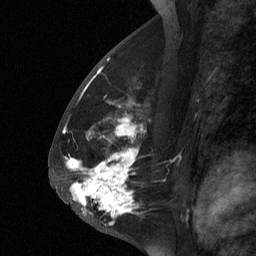
Breast MRI (dynamic contrast-enhanced), one sagittal slice. Position 34 of 64 along the scan axis. Dynamic contrast-enhanced study with each time point stored as its own series, time point 2 of 3 at this slice position (early post-contrast, ordered by acquisition time). 1.5 T. TE 4.8 ms, TR 27 ms. 2 mm slice thickness. 256 × 256 image matrix, field of view 180 × 180 mm. Female patient, age 56 years. Case-level facts recorded for this patient, not image findings: setting: breast cancer imaged before/during neoadjuvant chemotherapy; receptor status: HER2-positive.
Annotated regions visible in this slice (semi-automatically segmented with operator editing):
- analysis volume of interest (the breast-tissue region the enhancement analysis was run in; not a lesion): bounding box (x1, y1, x2, y2) in pixels: (59, 104, 152, 229)
- tumour enhancement mask (voxels above the 90 % enhancement threshold inside the analysis volume of interest): (70, 164, 133, 215)